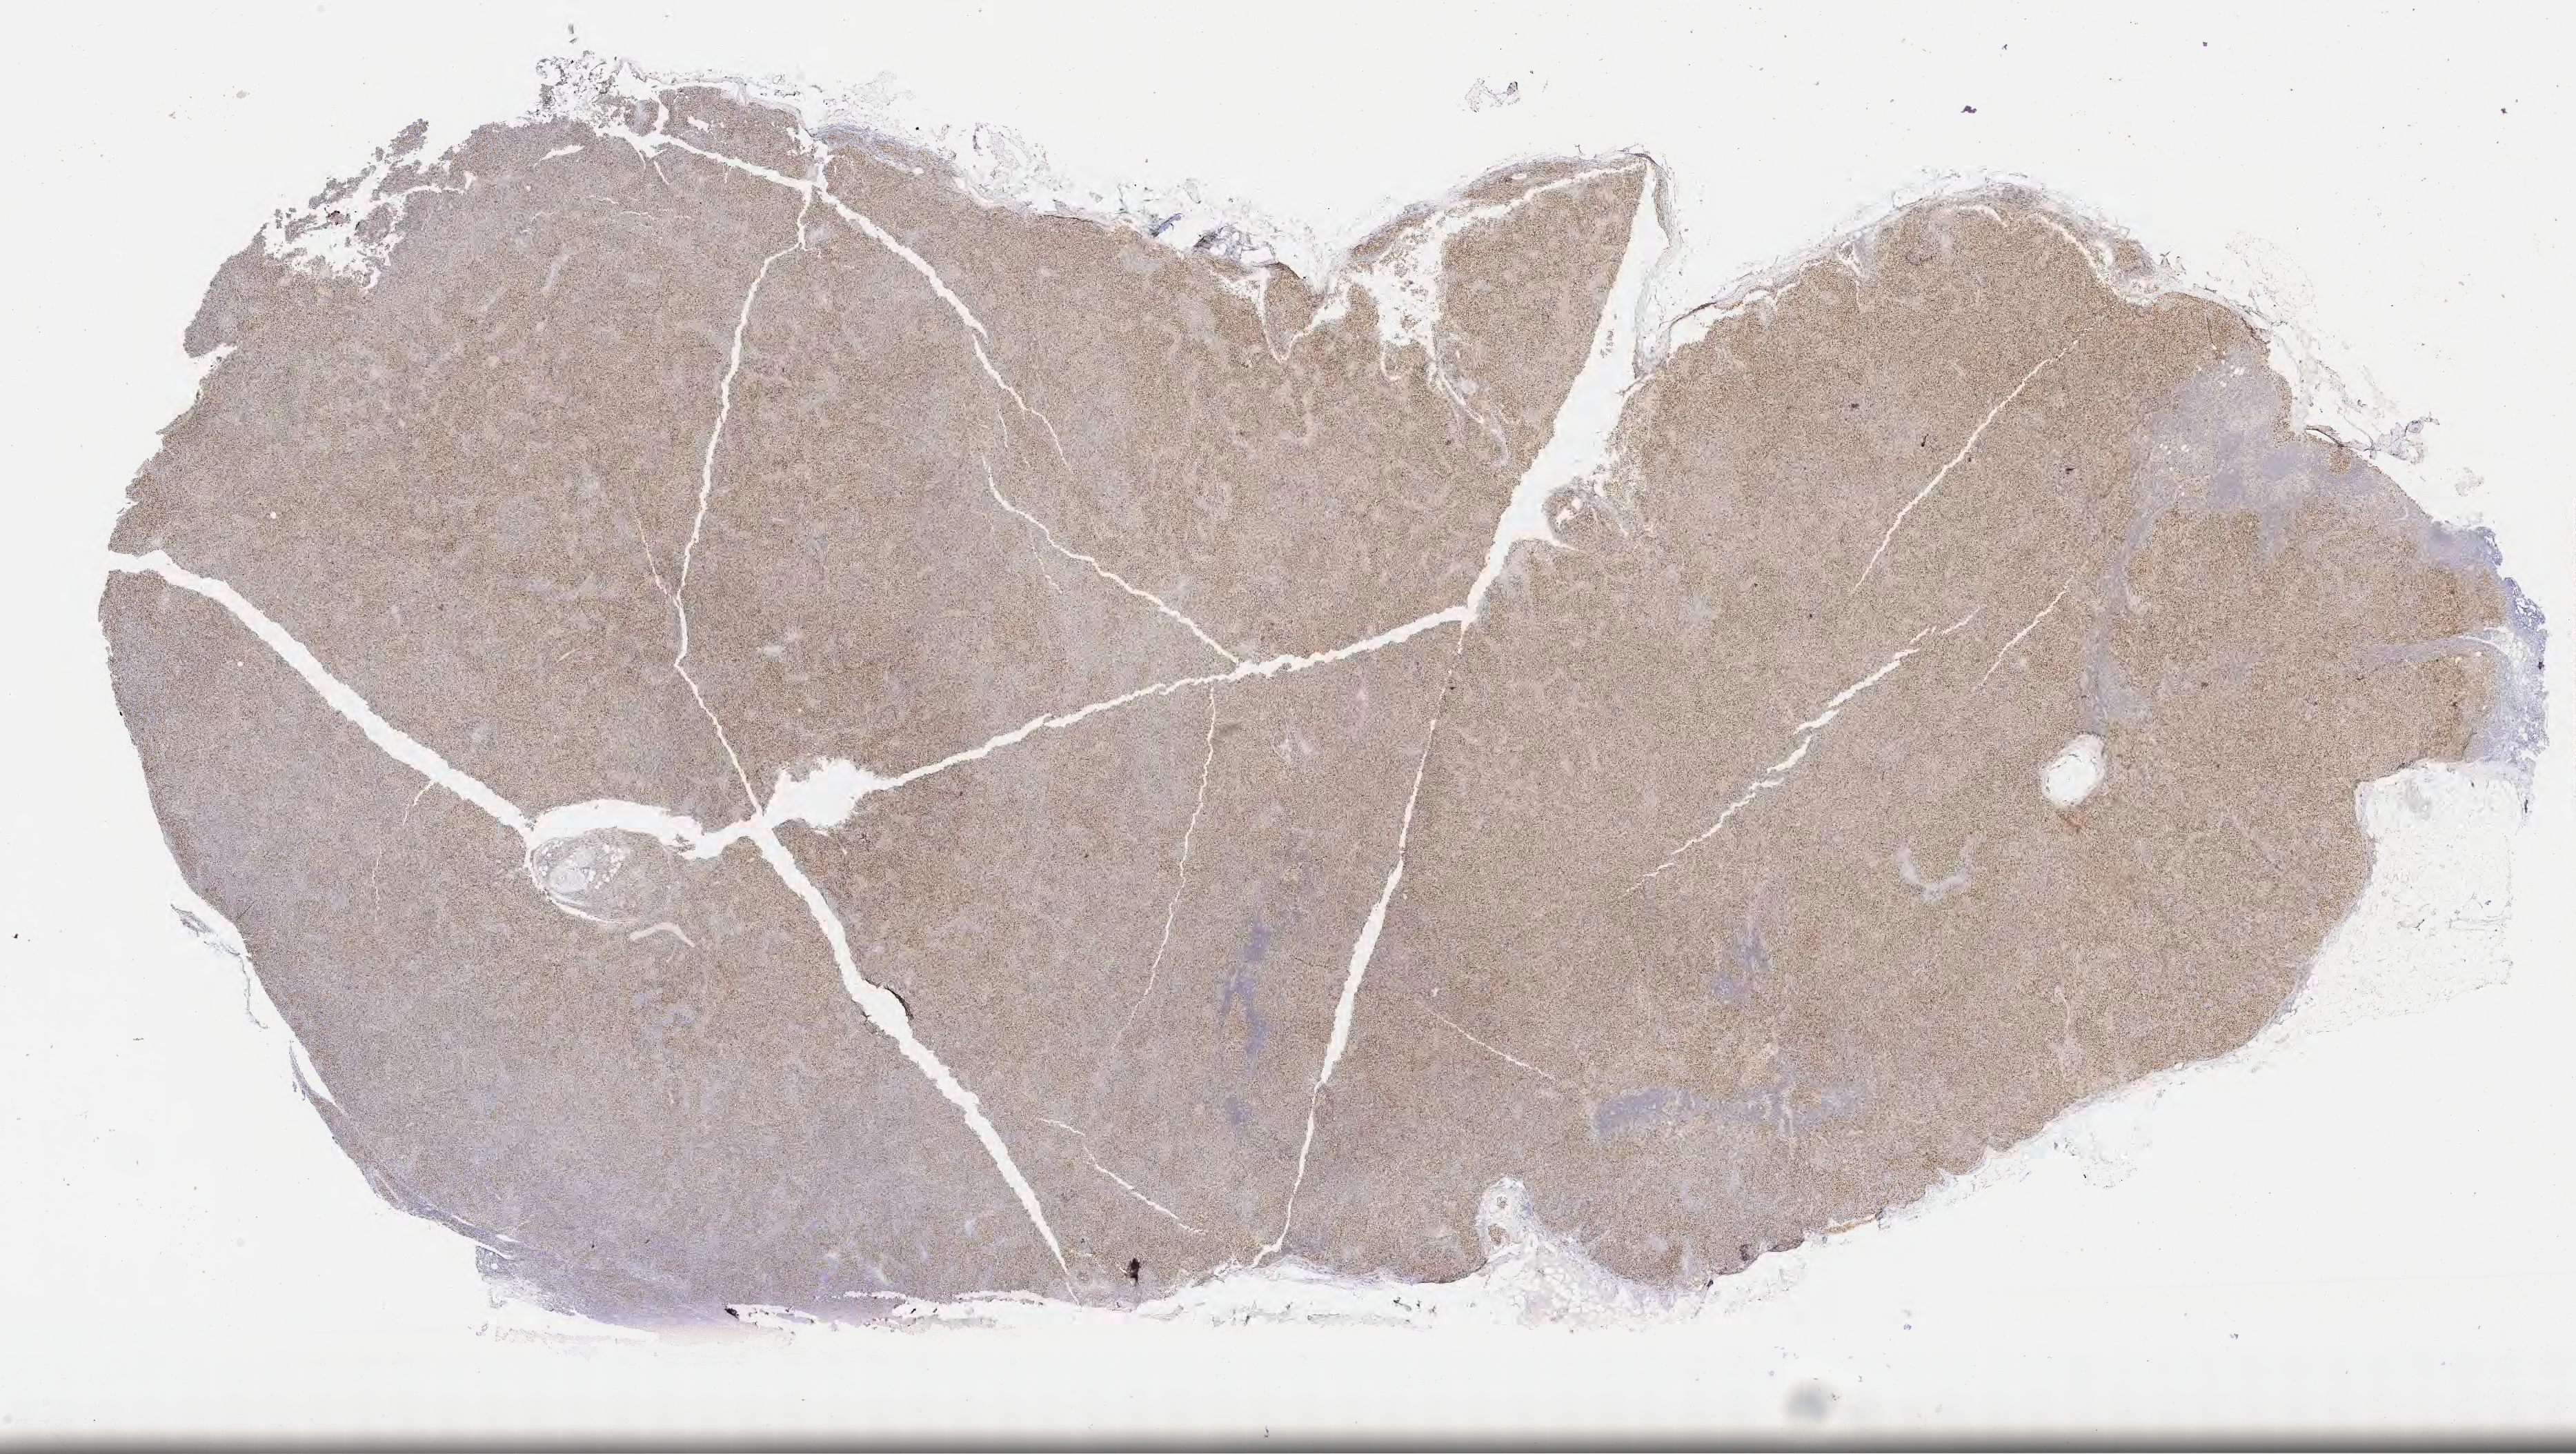
Immunohistochemistry (IHC) whole-slide image stained for BCL6, whole scanned area (about 30.2 x 17.1 mm) shown as a low-resolution overview, tumor tissue. Male patient, age 69 years.
Histologic diagnosis: Diffuse large B-cell lymphoma, NOS.